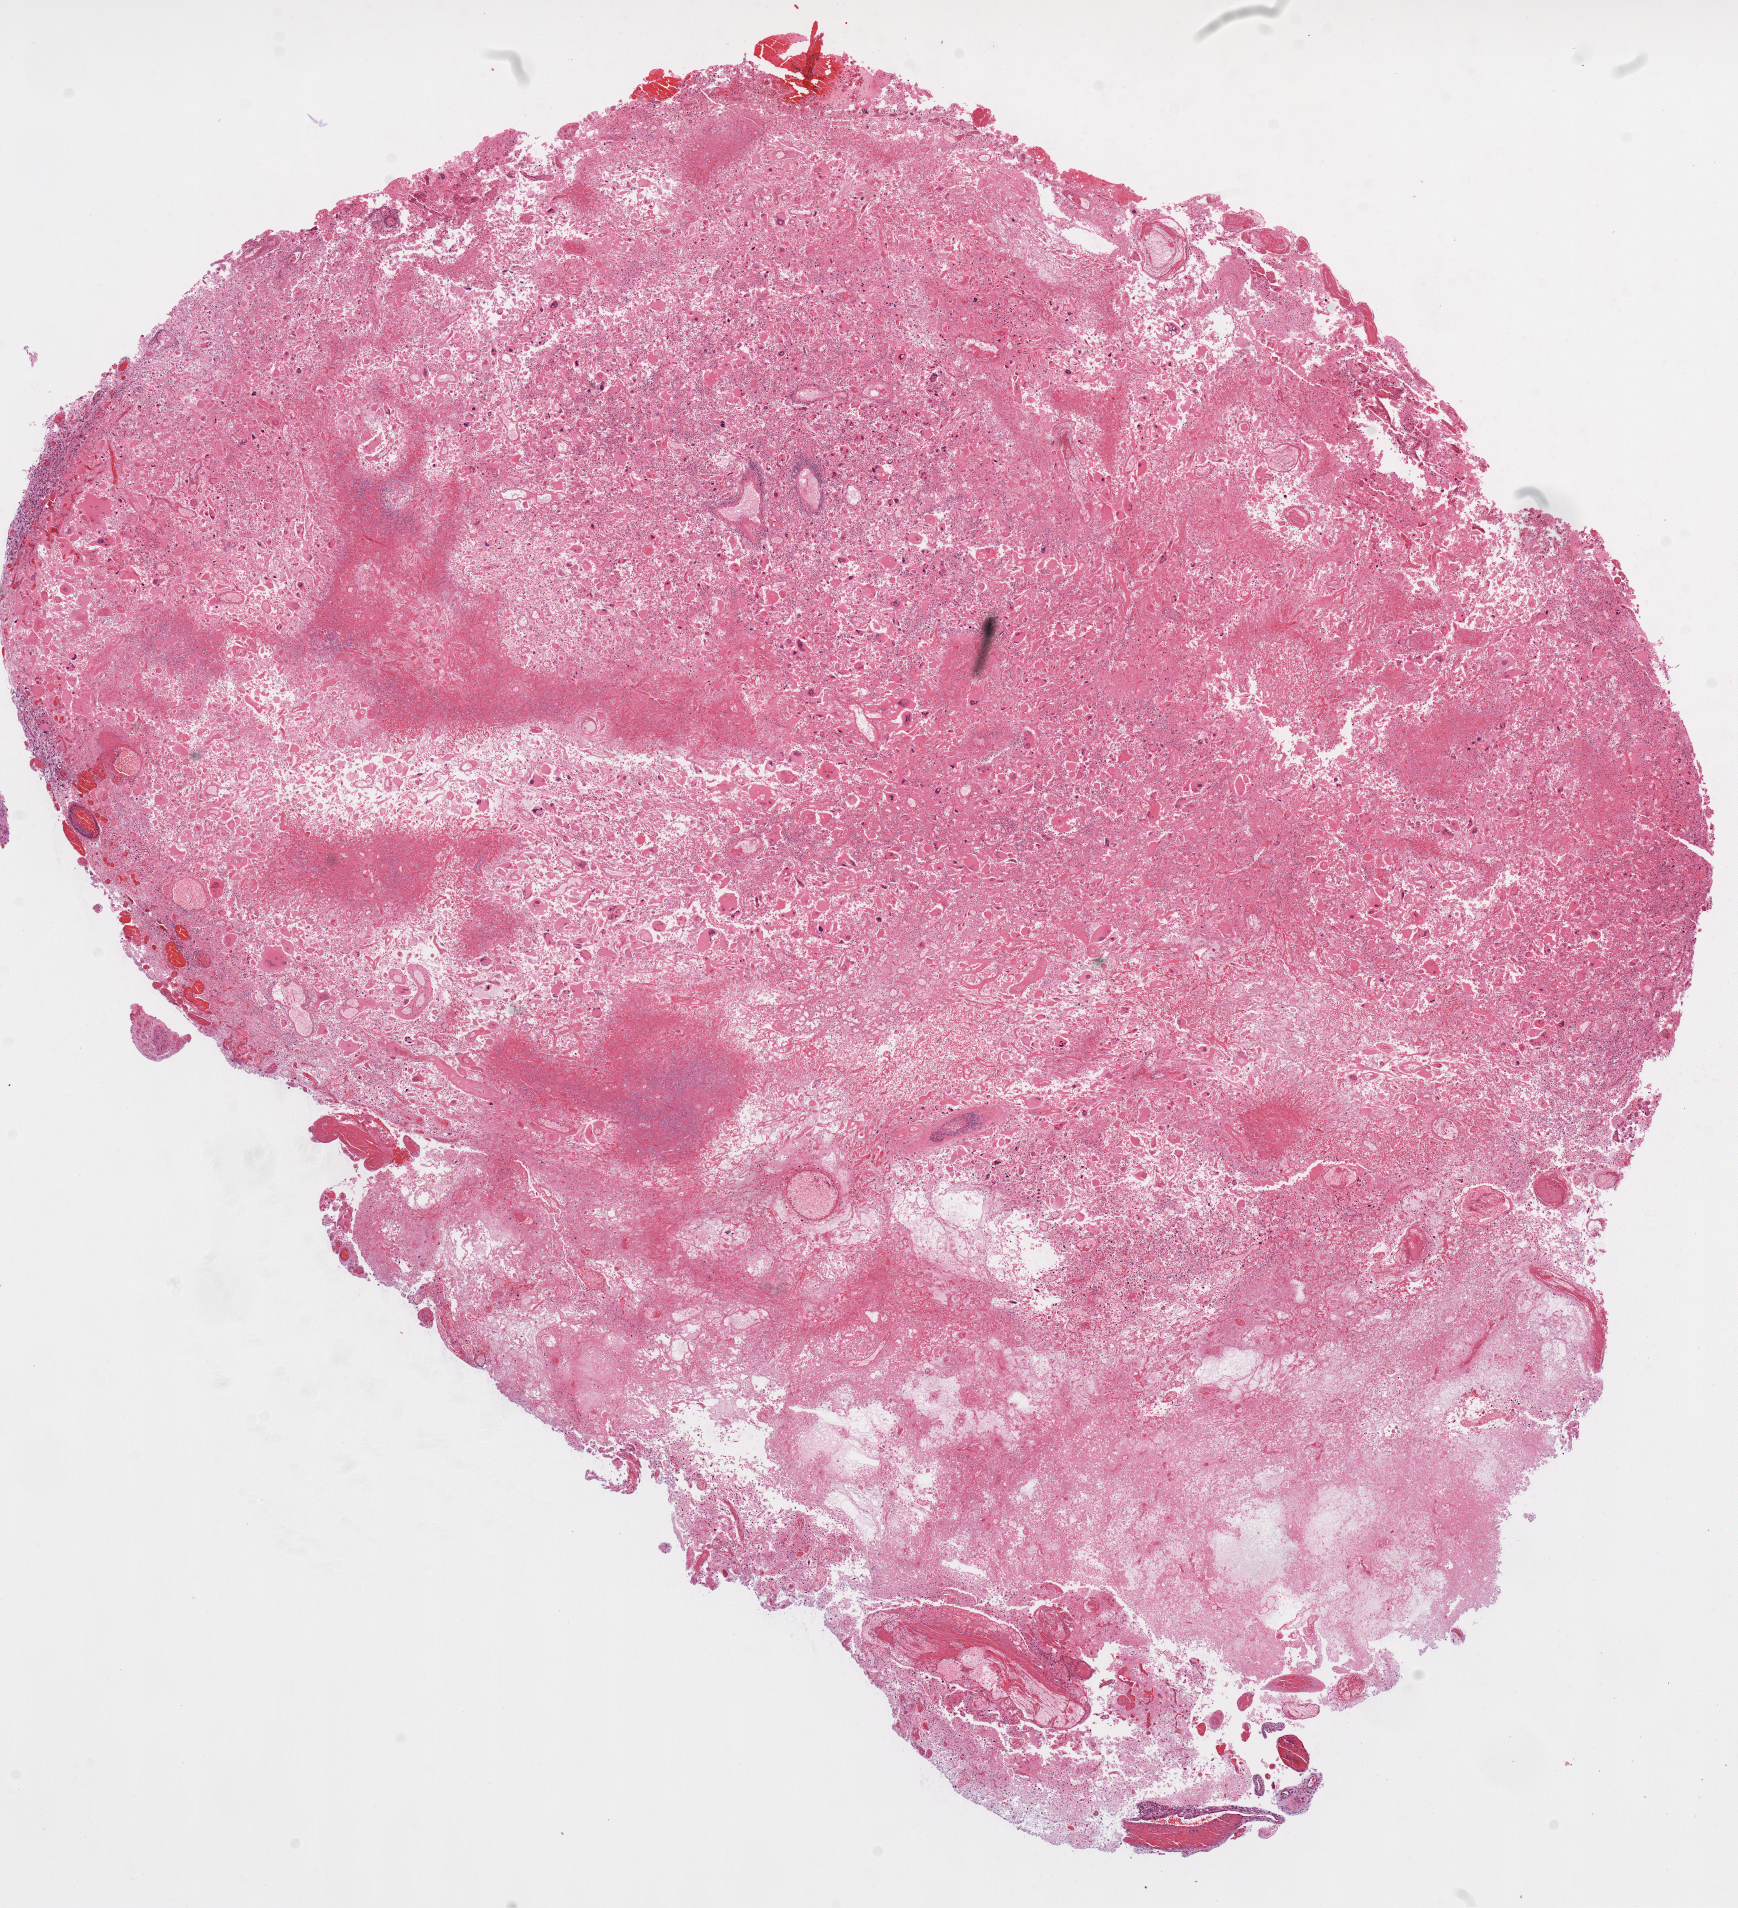
Digitized H&E tissue section (whole slide), whole scanned area (about 14.0 x 15.4 mm, acquisition: 20x scan) shown as a low-resolution overview, formalin-fixed paraffin-embedded (FFPE) diagnostic section, primary tumour sample from the brain. Female, age 55 years at initial diagnosis.
Histologic diagnosis: Glioblastoma.